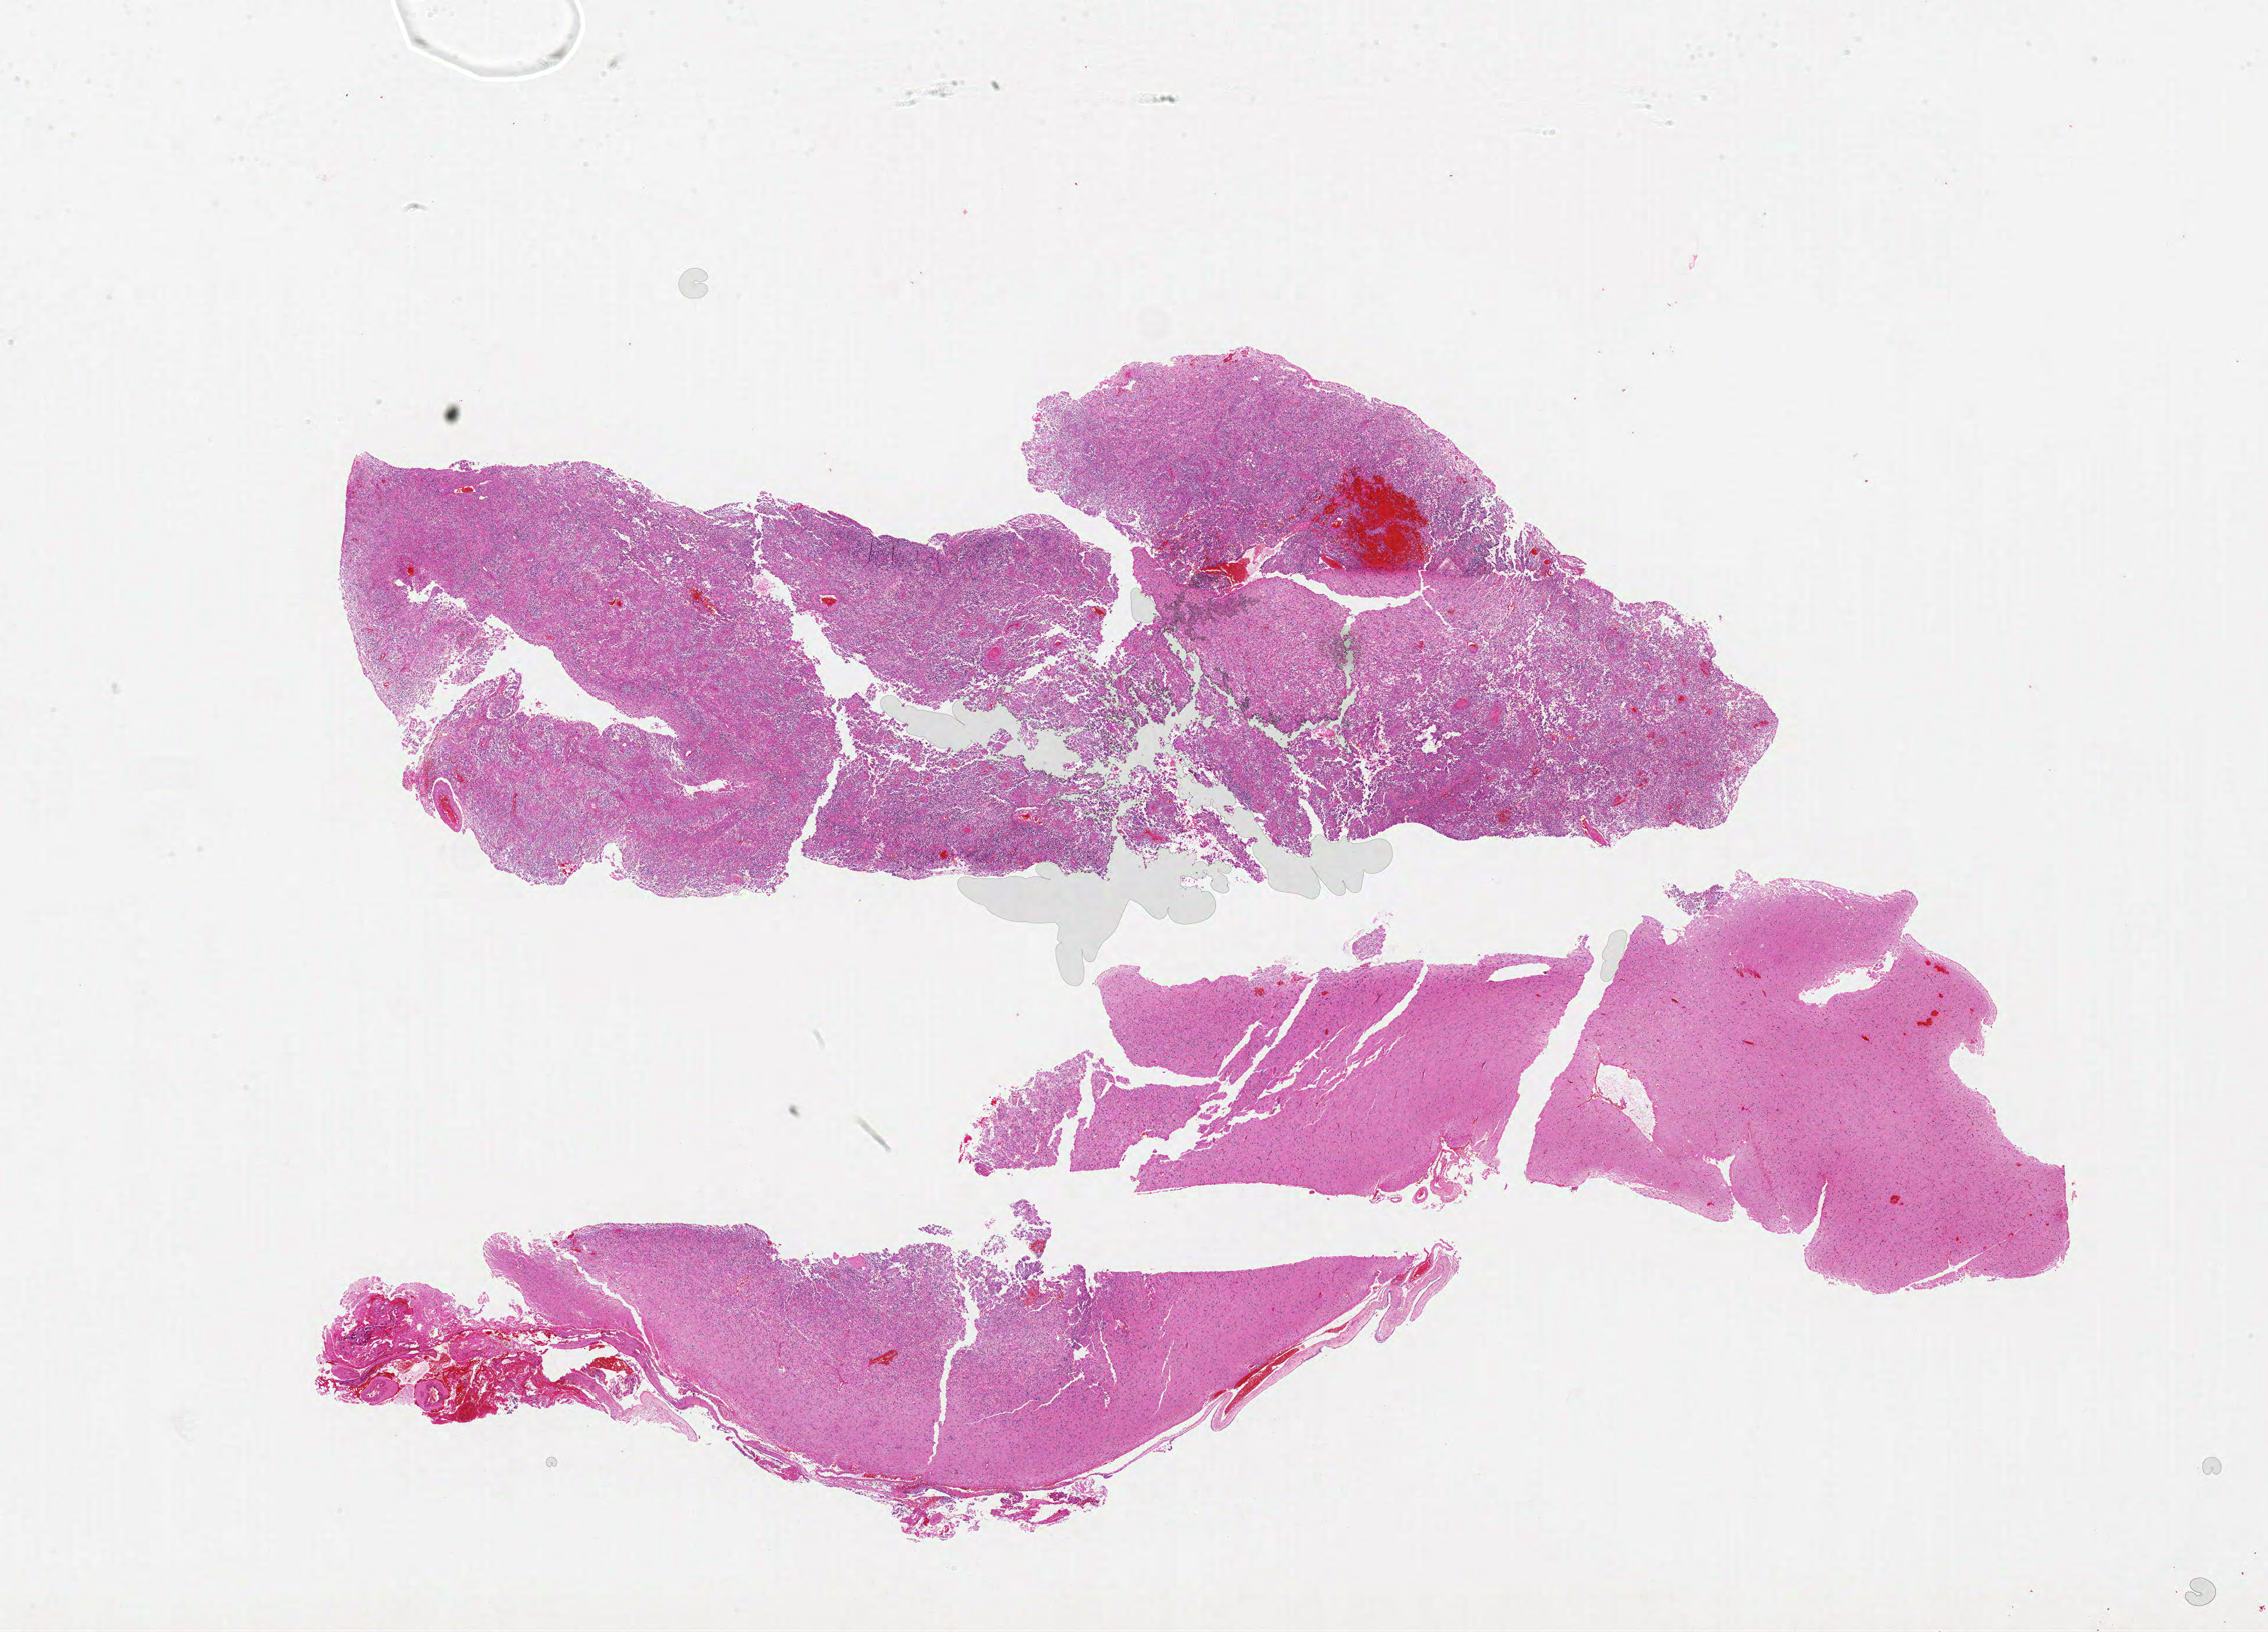
Whole-slide histology image, Hematoxylin and eosin (H&E) stained — shown as a low-resolution overview of the whole scanned area (about 31.0 x 22.3 mm, from a 20x scan); formalin-fixed paraffin-embedded (FFPE) diagnostic section; primary tumour sample from the brain. Male patient; age at initial diagnosis 58 years.
Histologic diagnosis: Glioblastoma.